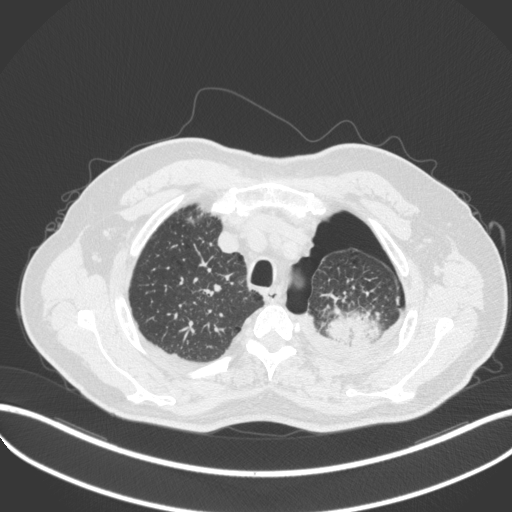
Chest CT, one axial slice. Position 413 of 466 along the scan axis. Reconstruction kernel B31f. Lung window (W 1500 / L -600 HU). 512 × 512 image matrix, field of view 400 × 400 mm. Male patient, age 76 years. From the clinical record (not read from this slice): clinical TNM (as recorded): T3 N0 M1b.
Outlined on this slice (bounding box drawn by a radiologist):
- lung tumour (recorded histology: adenocarcinoma): bounding box [x1, y1, x2, y2] px = [323, 308, 385, 345]